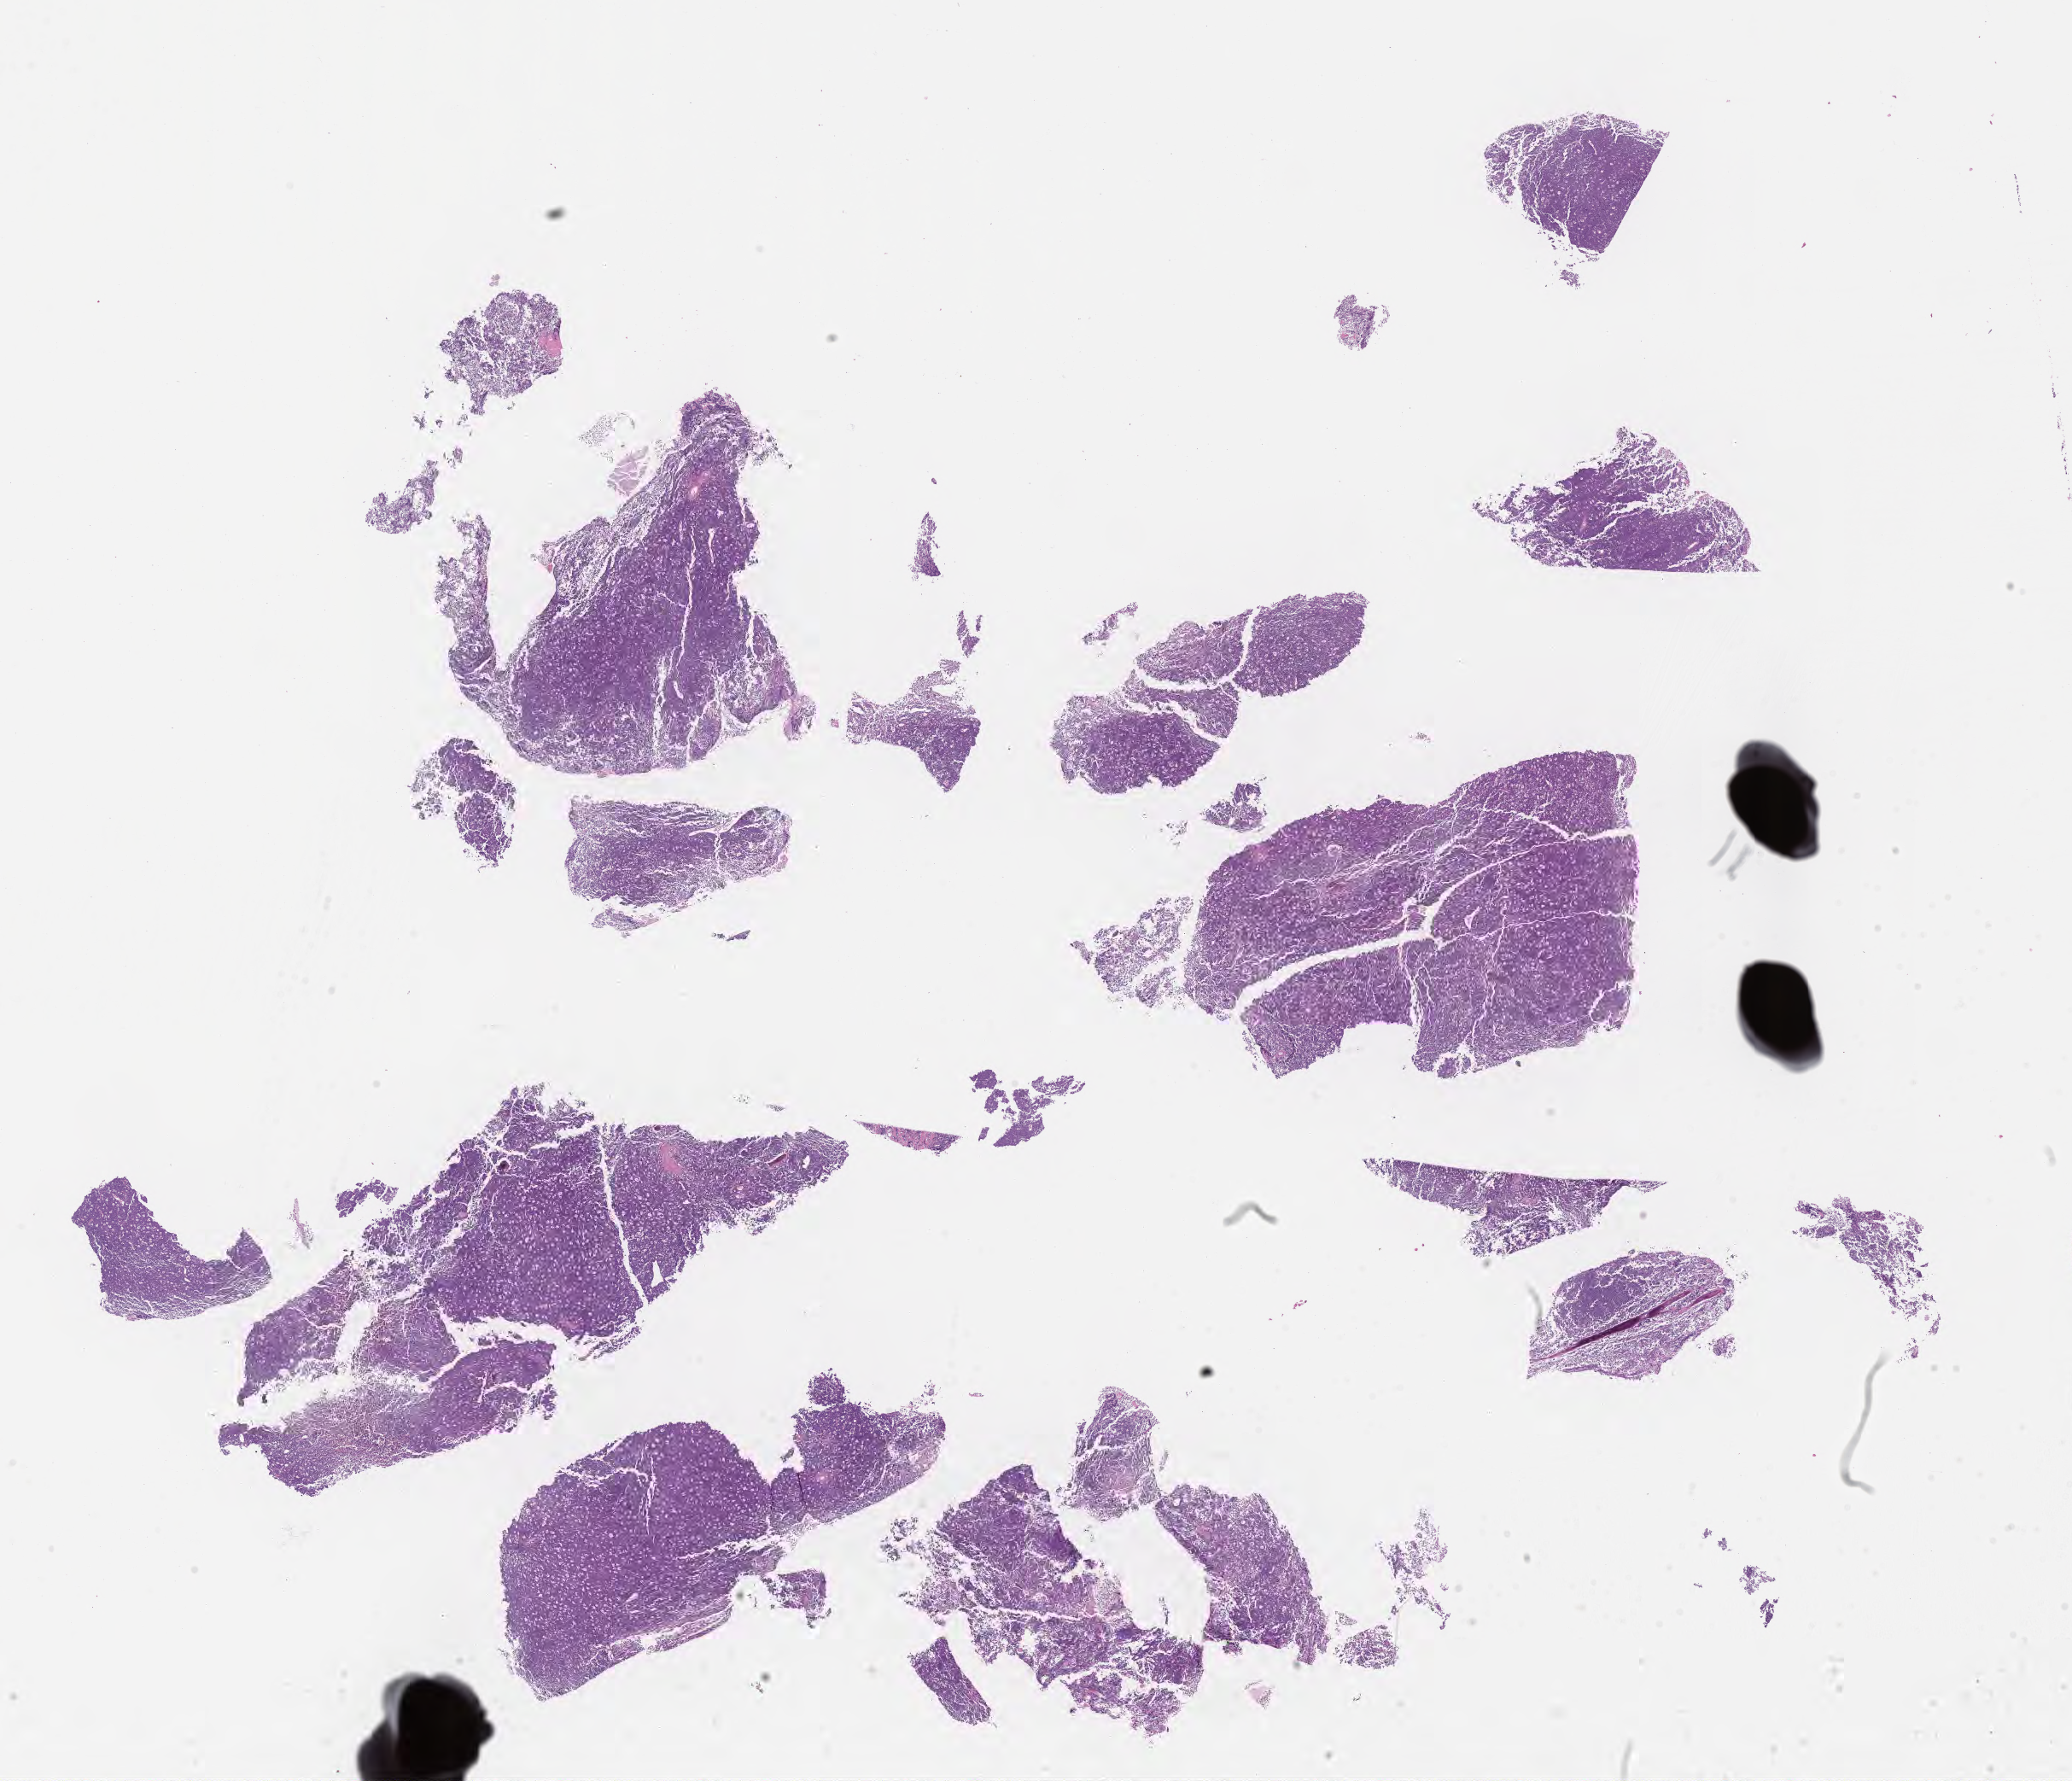
Whole-slide image, hematoxylin and eosin (H&E) stain, whole scanned area (about 19.6 x 16.9 mm) shown as a low-resolution overview, specimen: tumor tissue. Patient male; 11 years old.
- histologic diagnosis: Burkitt lymphoma, NOS